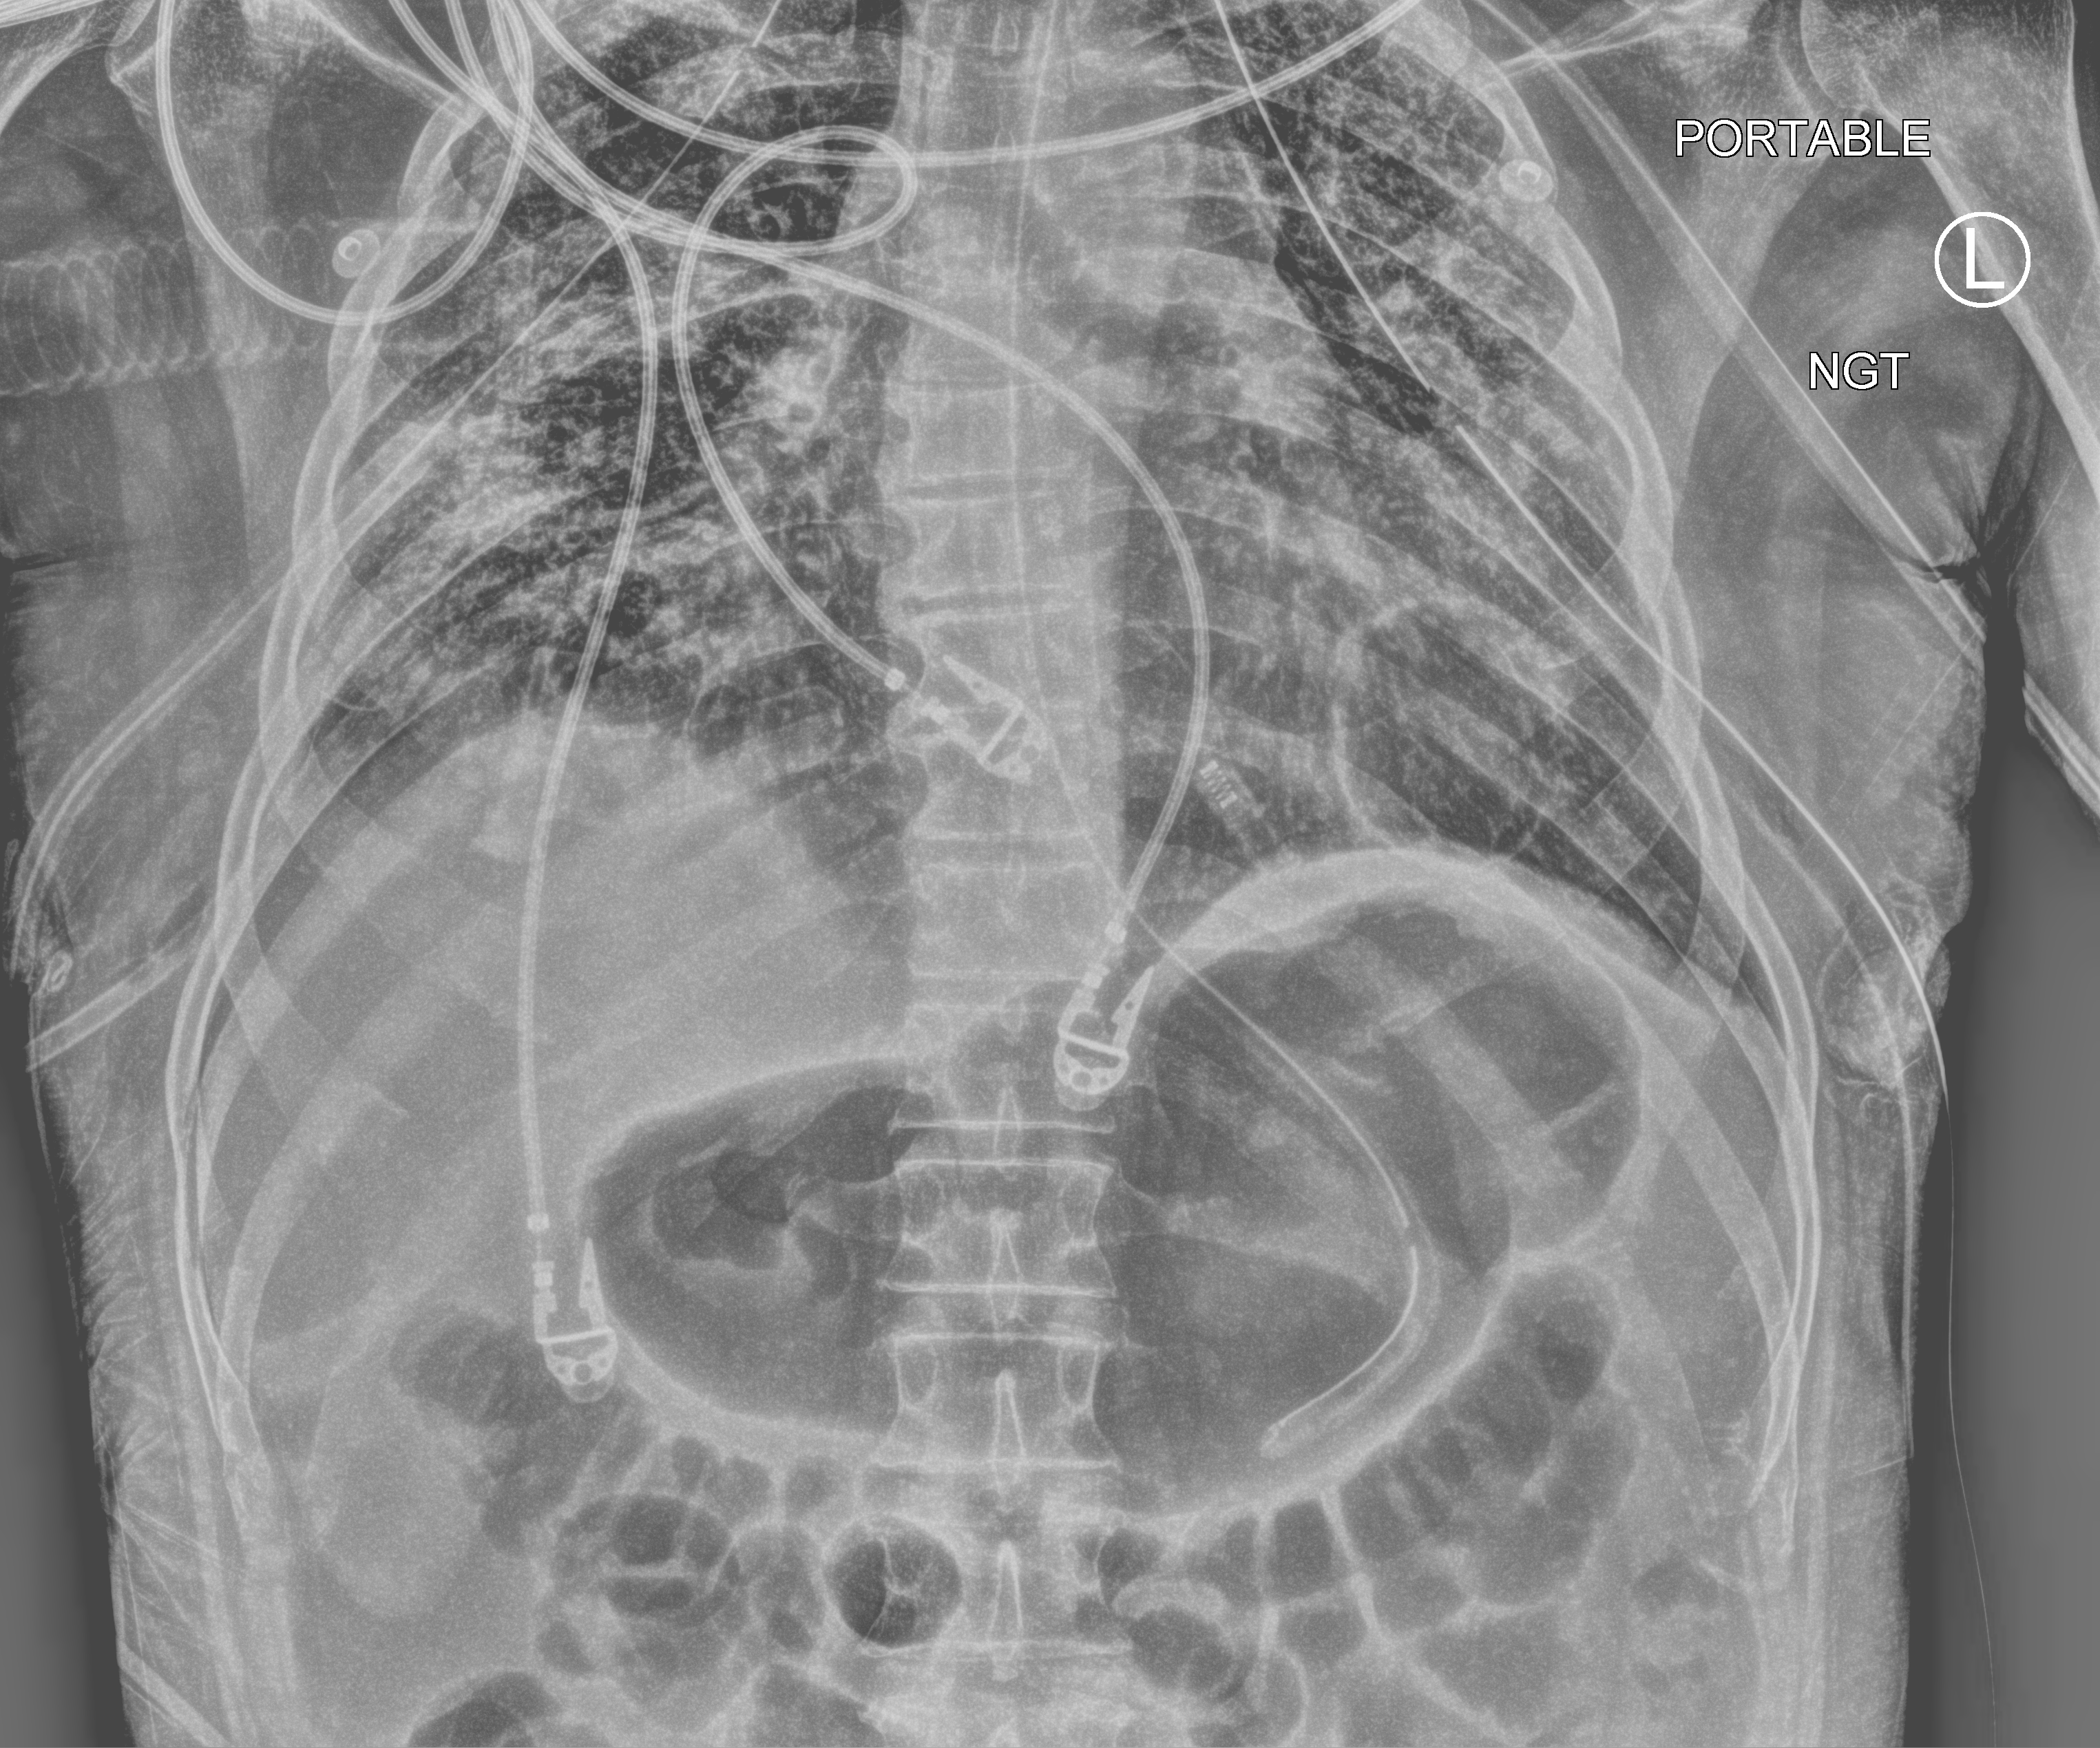
Portable chest radiograph; anteroposterior (AP) projection. Patient hospitalised with COVID-19; male, aged 18–59 years.
From the hospital-stay record, not from the radiograph (when in the stay this image was taken is not recorded): other chronic lung disease (admission record): no; mechanically ventilated during this hospital stay: yes.